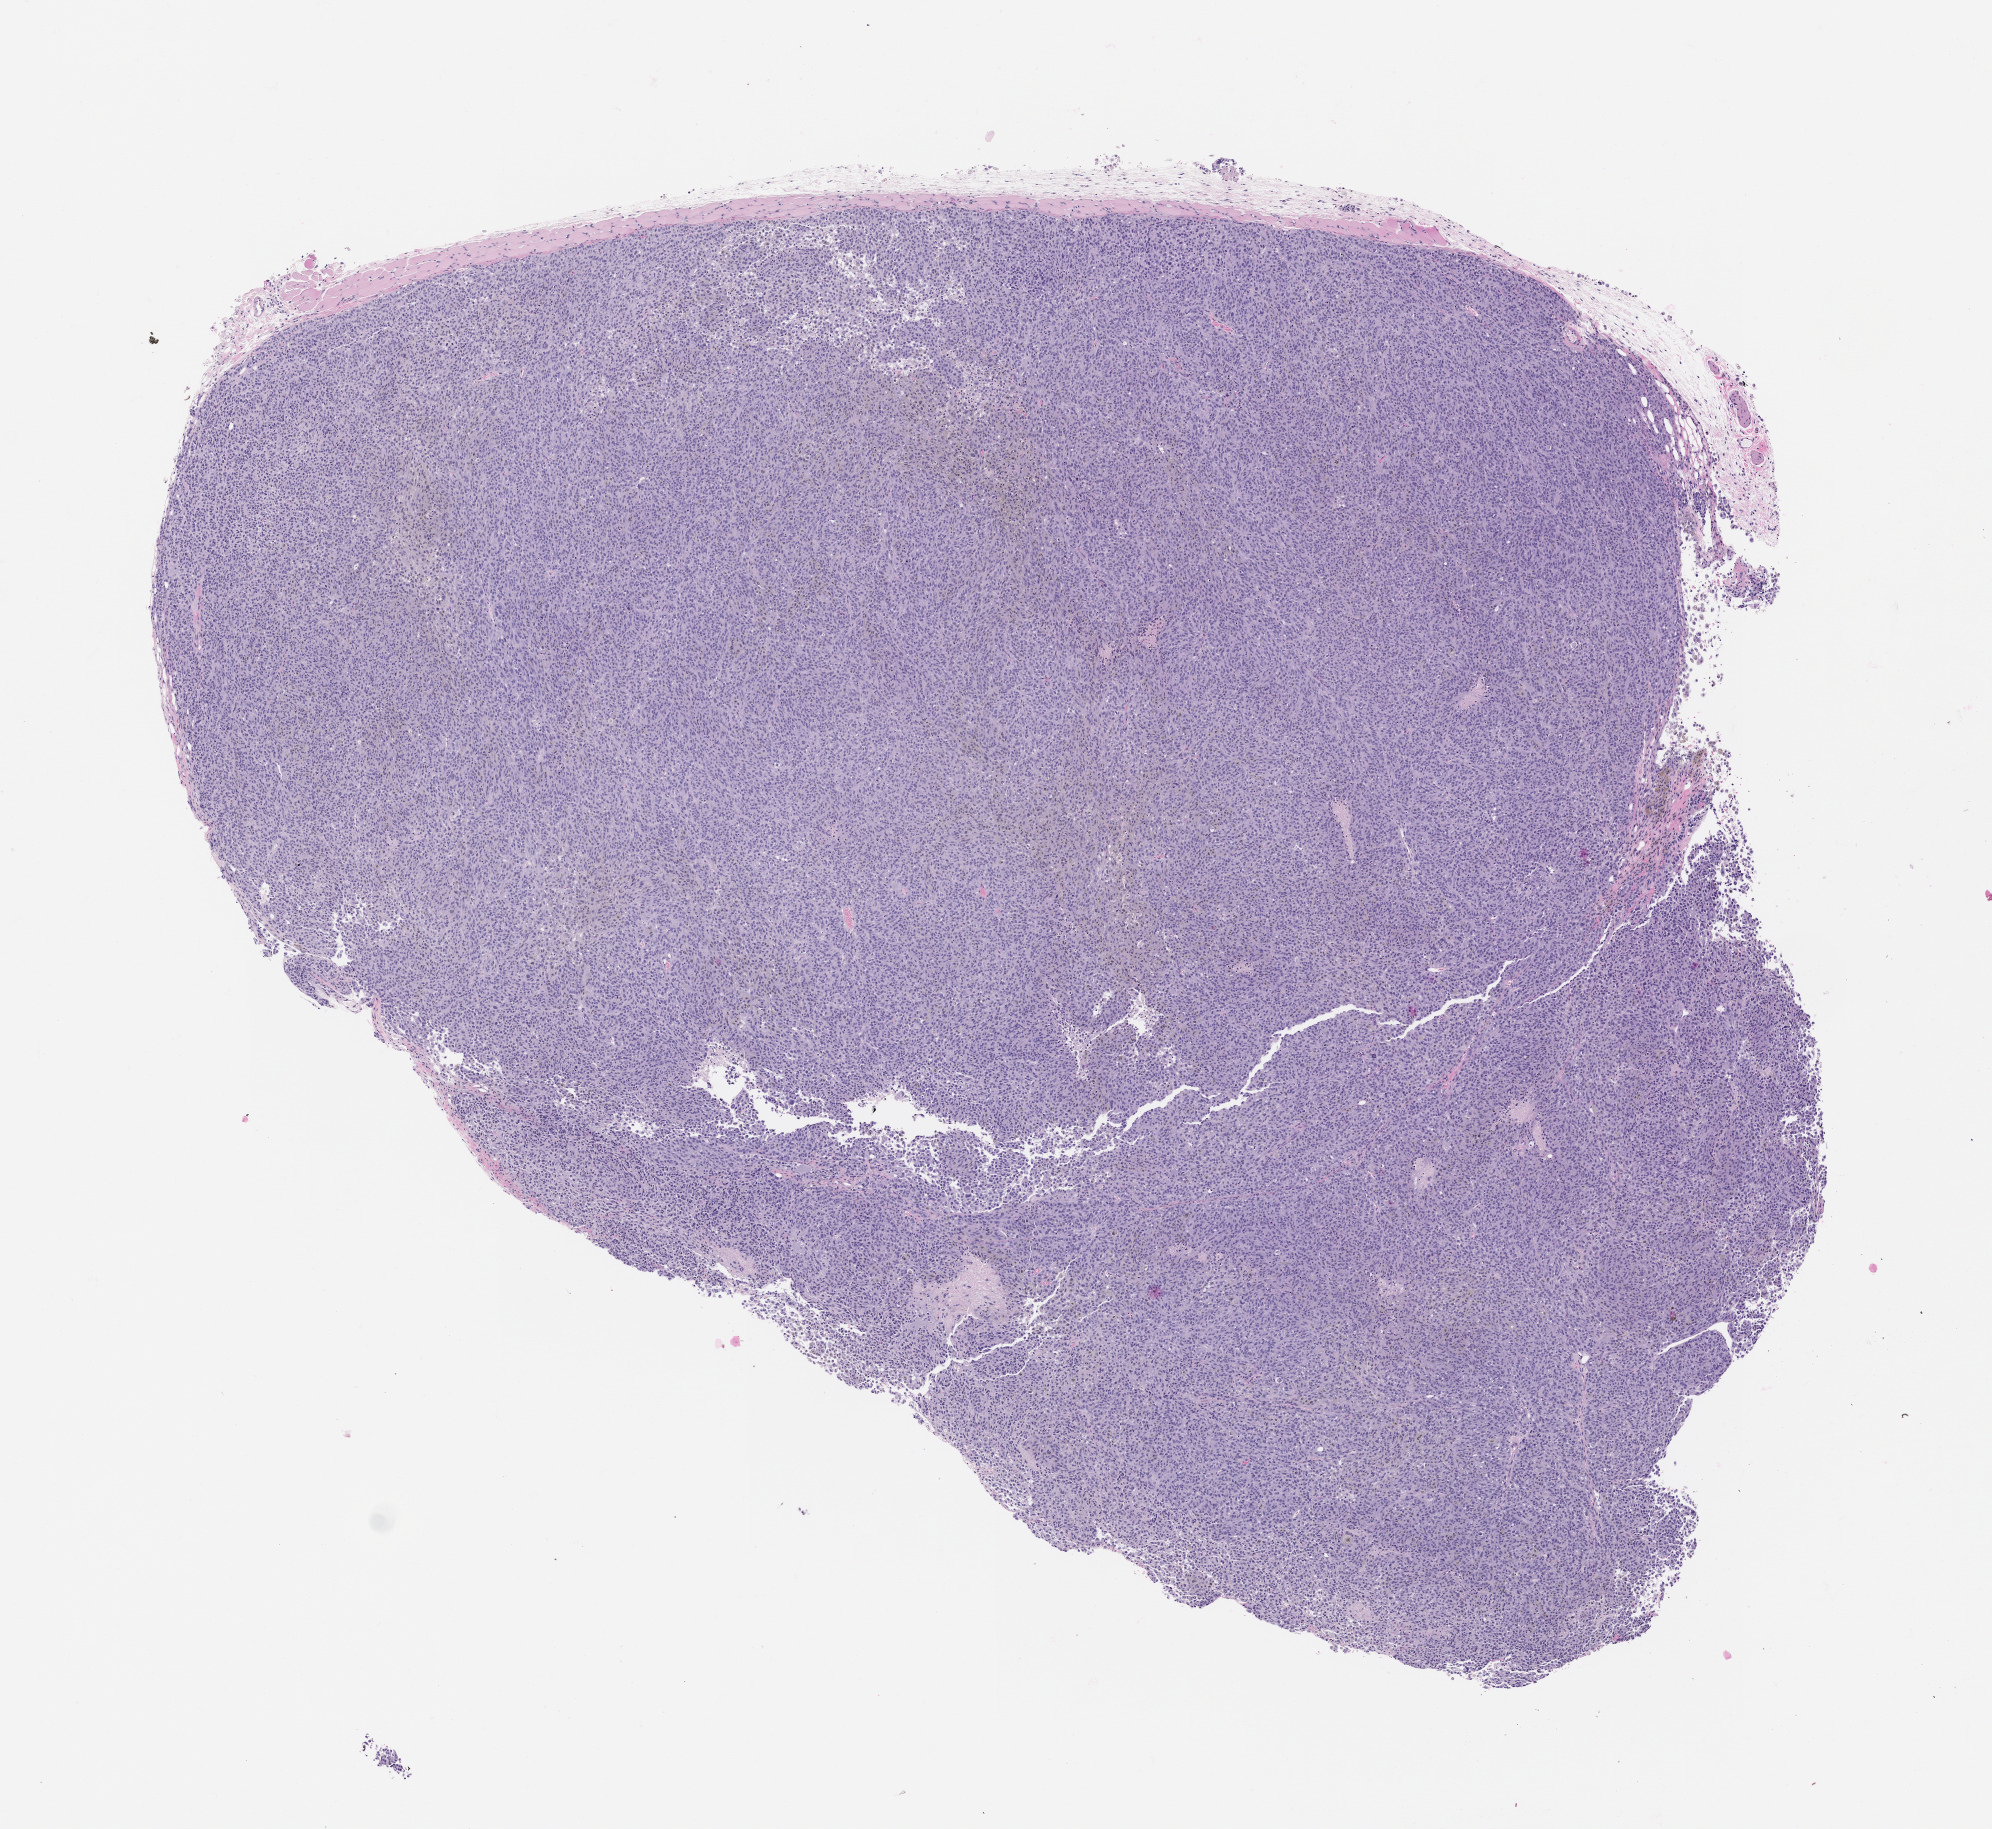
H&E whole-slide image of a patient-derived xenograft (PDX) tumor grown in a mouse, passage 1 — shown as a low-resolution overview of the whole scanned area (about 8.0 x 7.4 mm), FFPE section, tumor site category: skin.
Originating patient diagnosis: Melanoma.